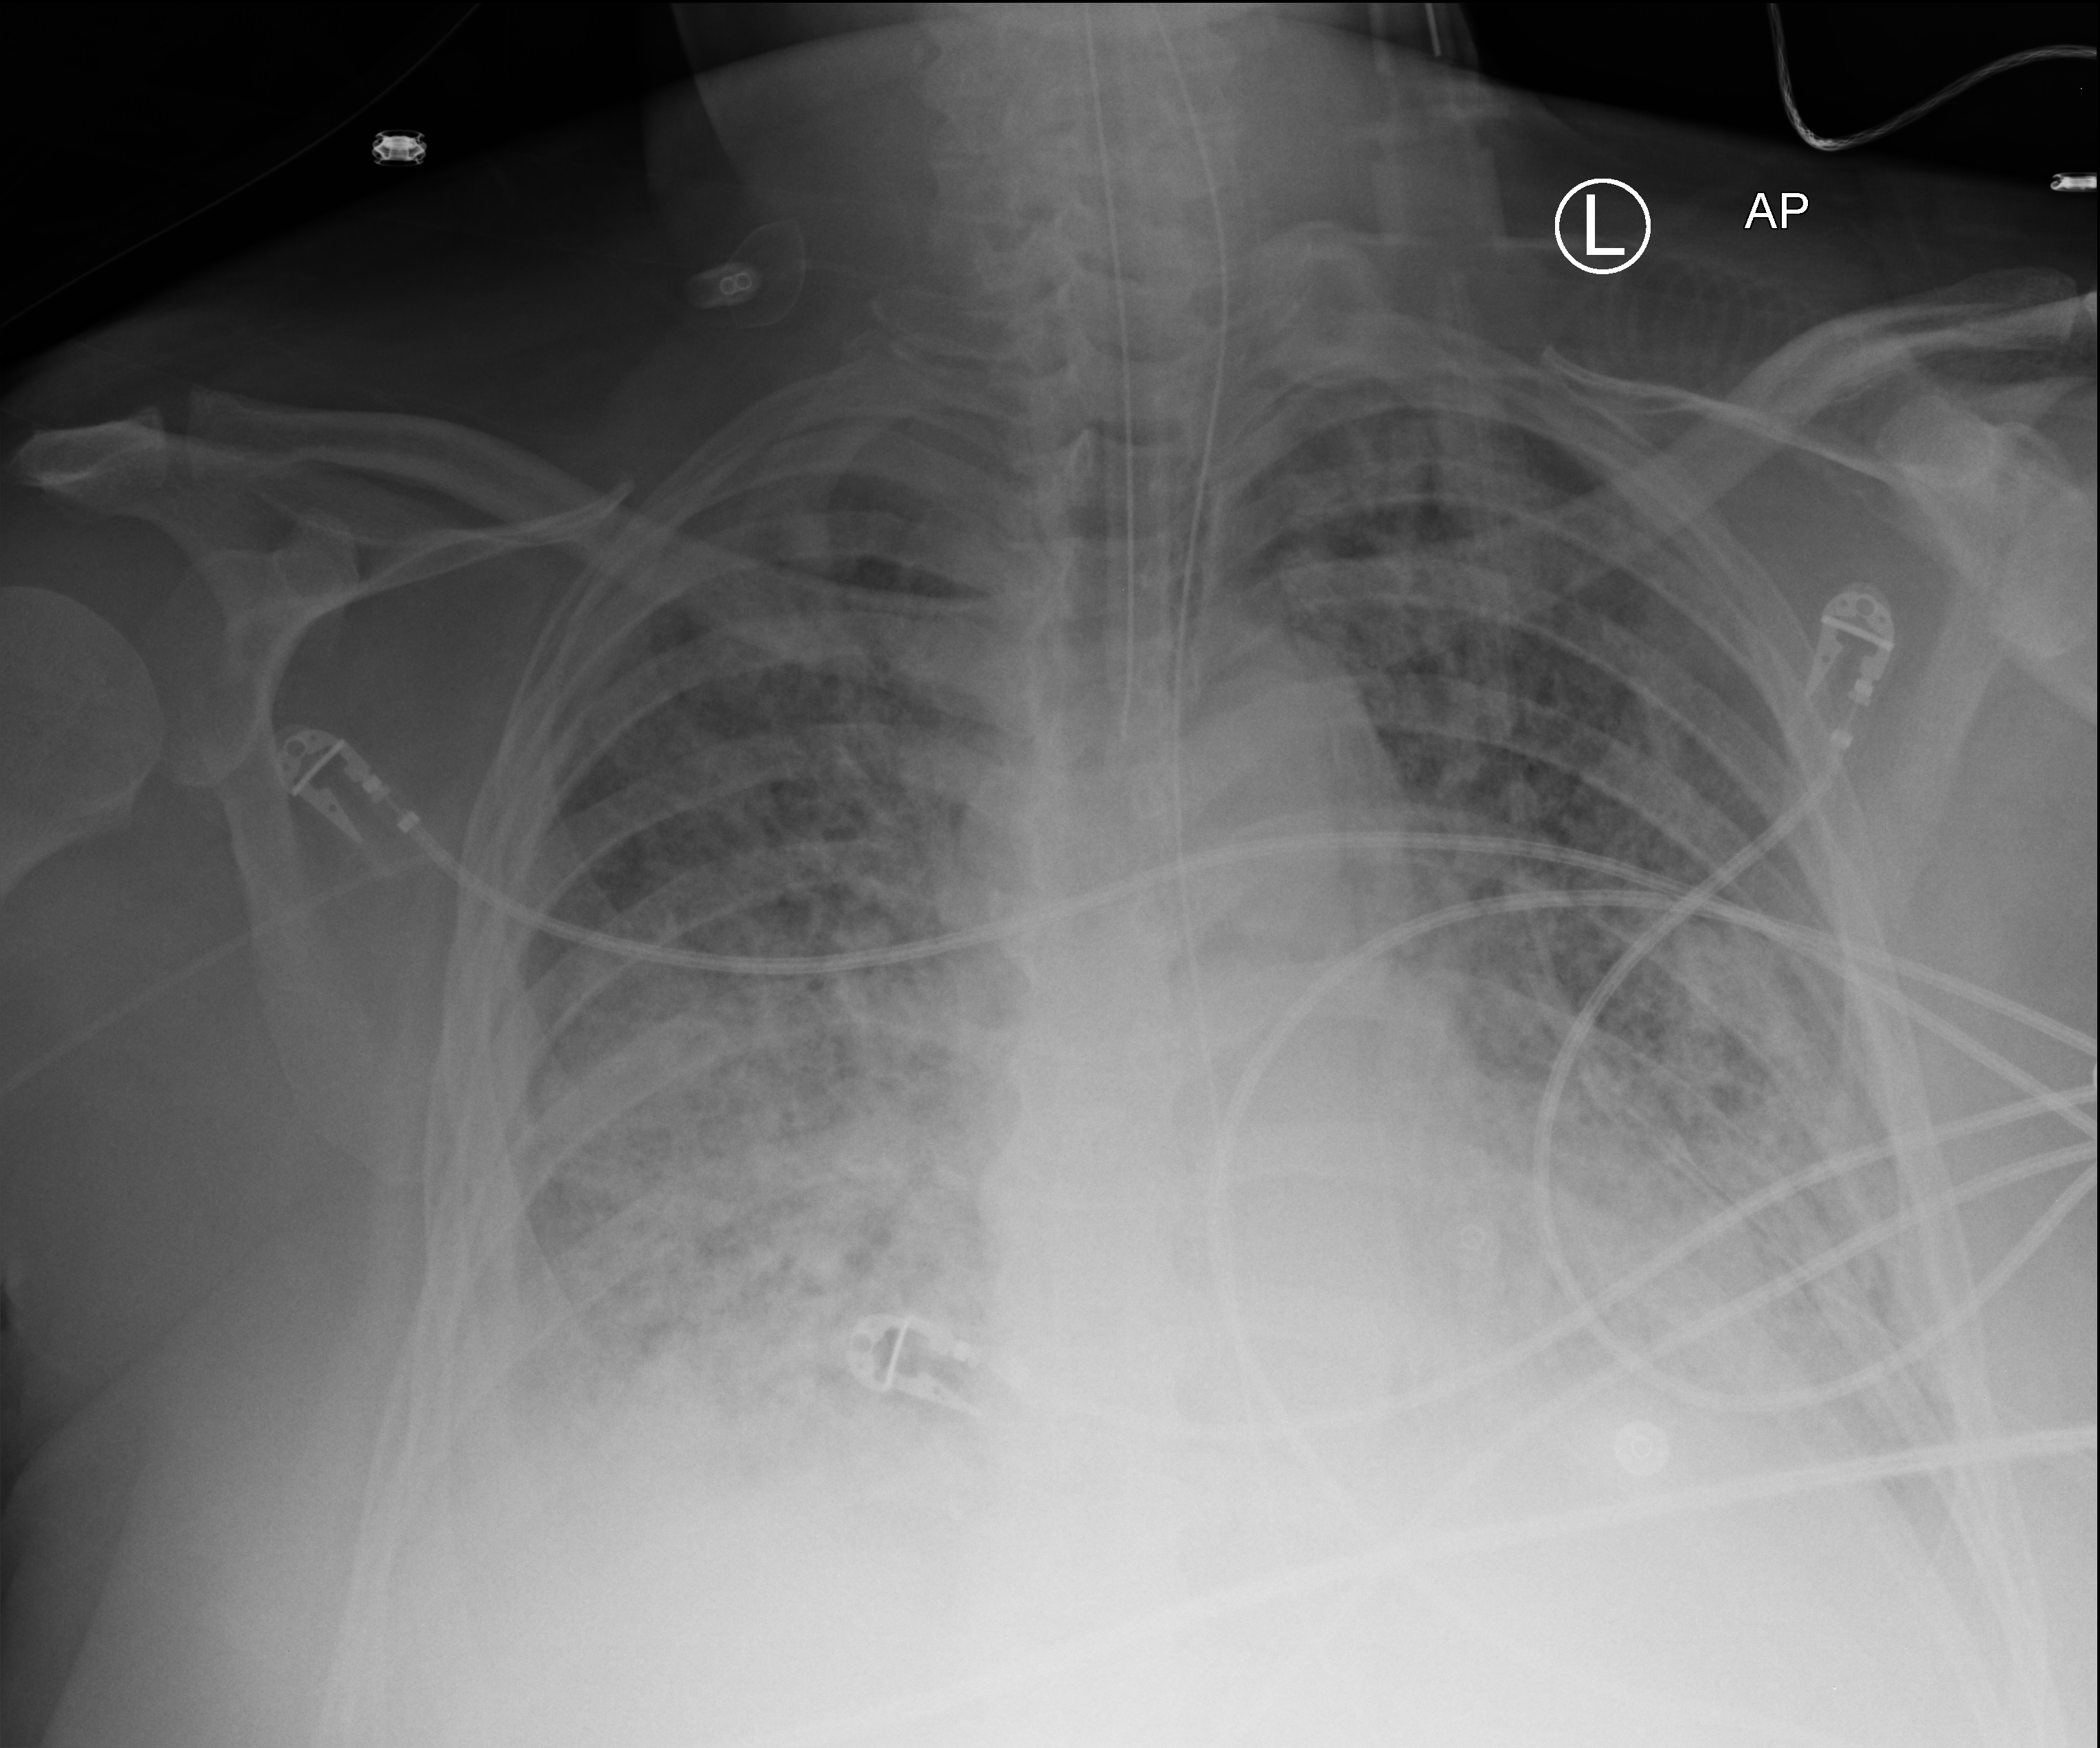
Chest X-ray (portable). Patient hospitalised with COVID-19; male, aged 60–74 years.
Hospital-stay facts (about this admission, not read from this image; timing relative to this image not recorded): admitted to intensive care during this hospital stay: yes.